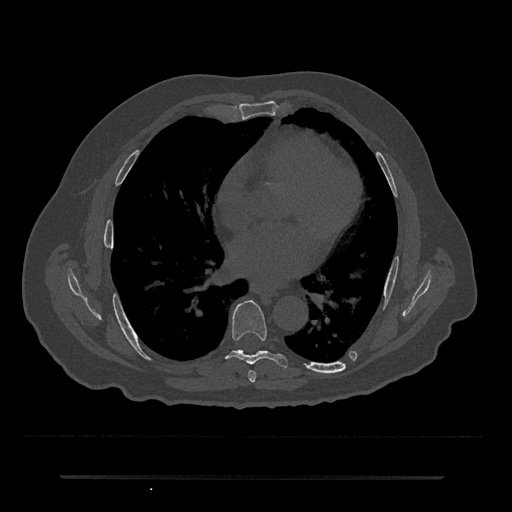
CT including the spine, one axial slice; position 385 of 797 along the scan axis; reconstruction kernel Br40s/3; 120 kVp; bone window (W 1800 / L 400 HU); 0.5 mm slice thickness; 512 × 512 image matrix, field of view 437 × 437 mm. Patient: male, 69 years. Case-level facts recorded for this patient, not image findings: primary cancer: prostate.
Annotated regions visible in this slice (semi-automatically segmented with operator editing):
- T6 vertebra: bounding box <248,370,256,383> (left, top, right, bottom; pixels)
- T7 vertebra: <226,300,288,368>